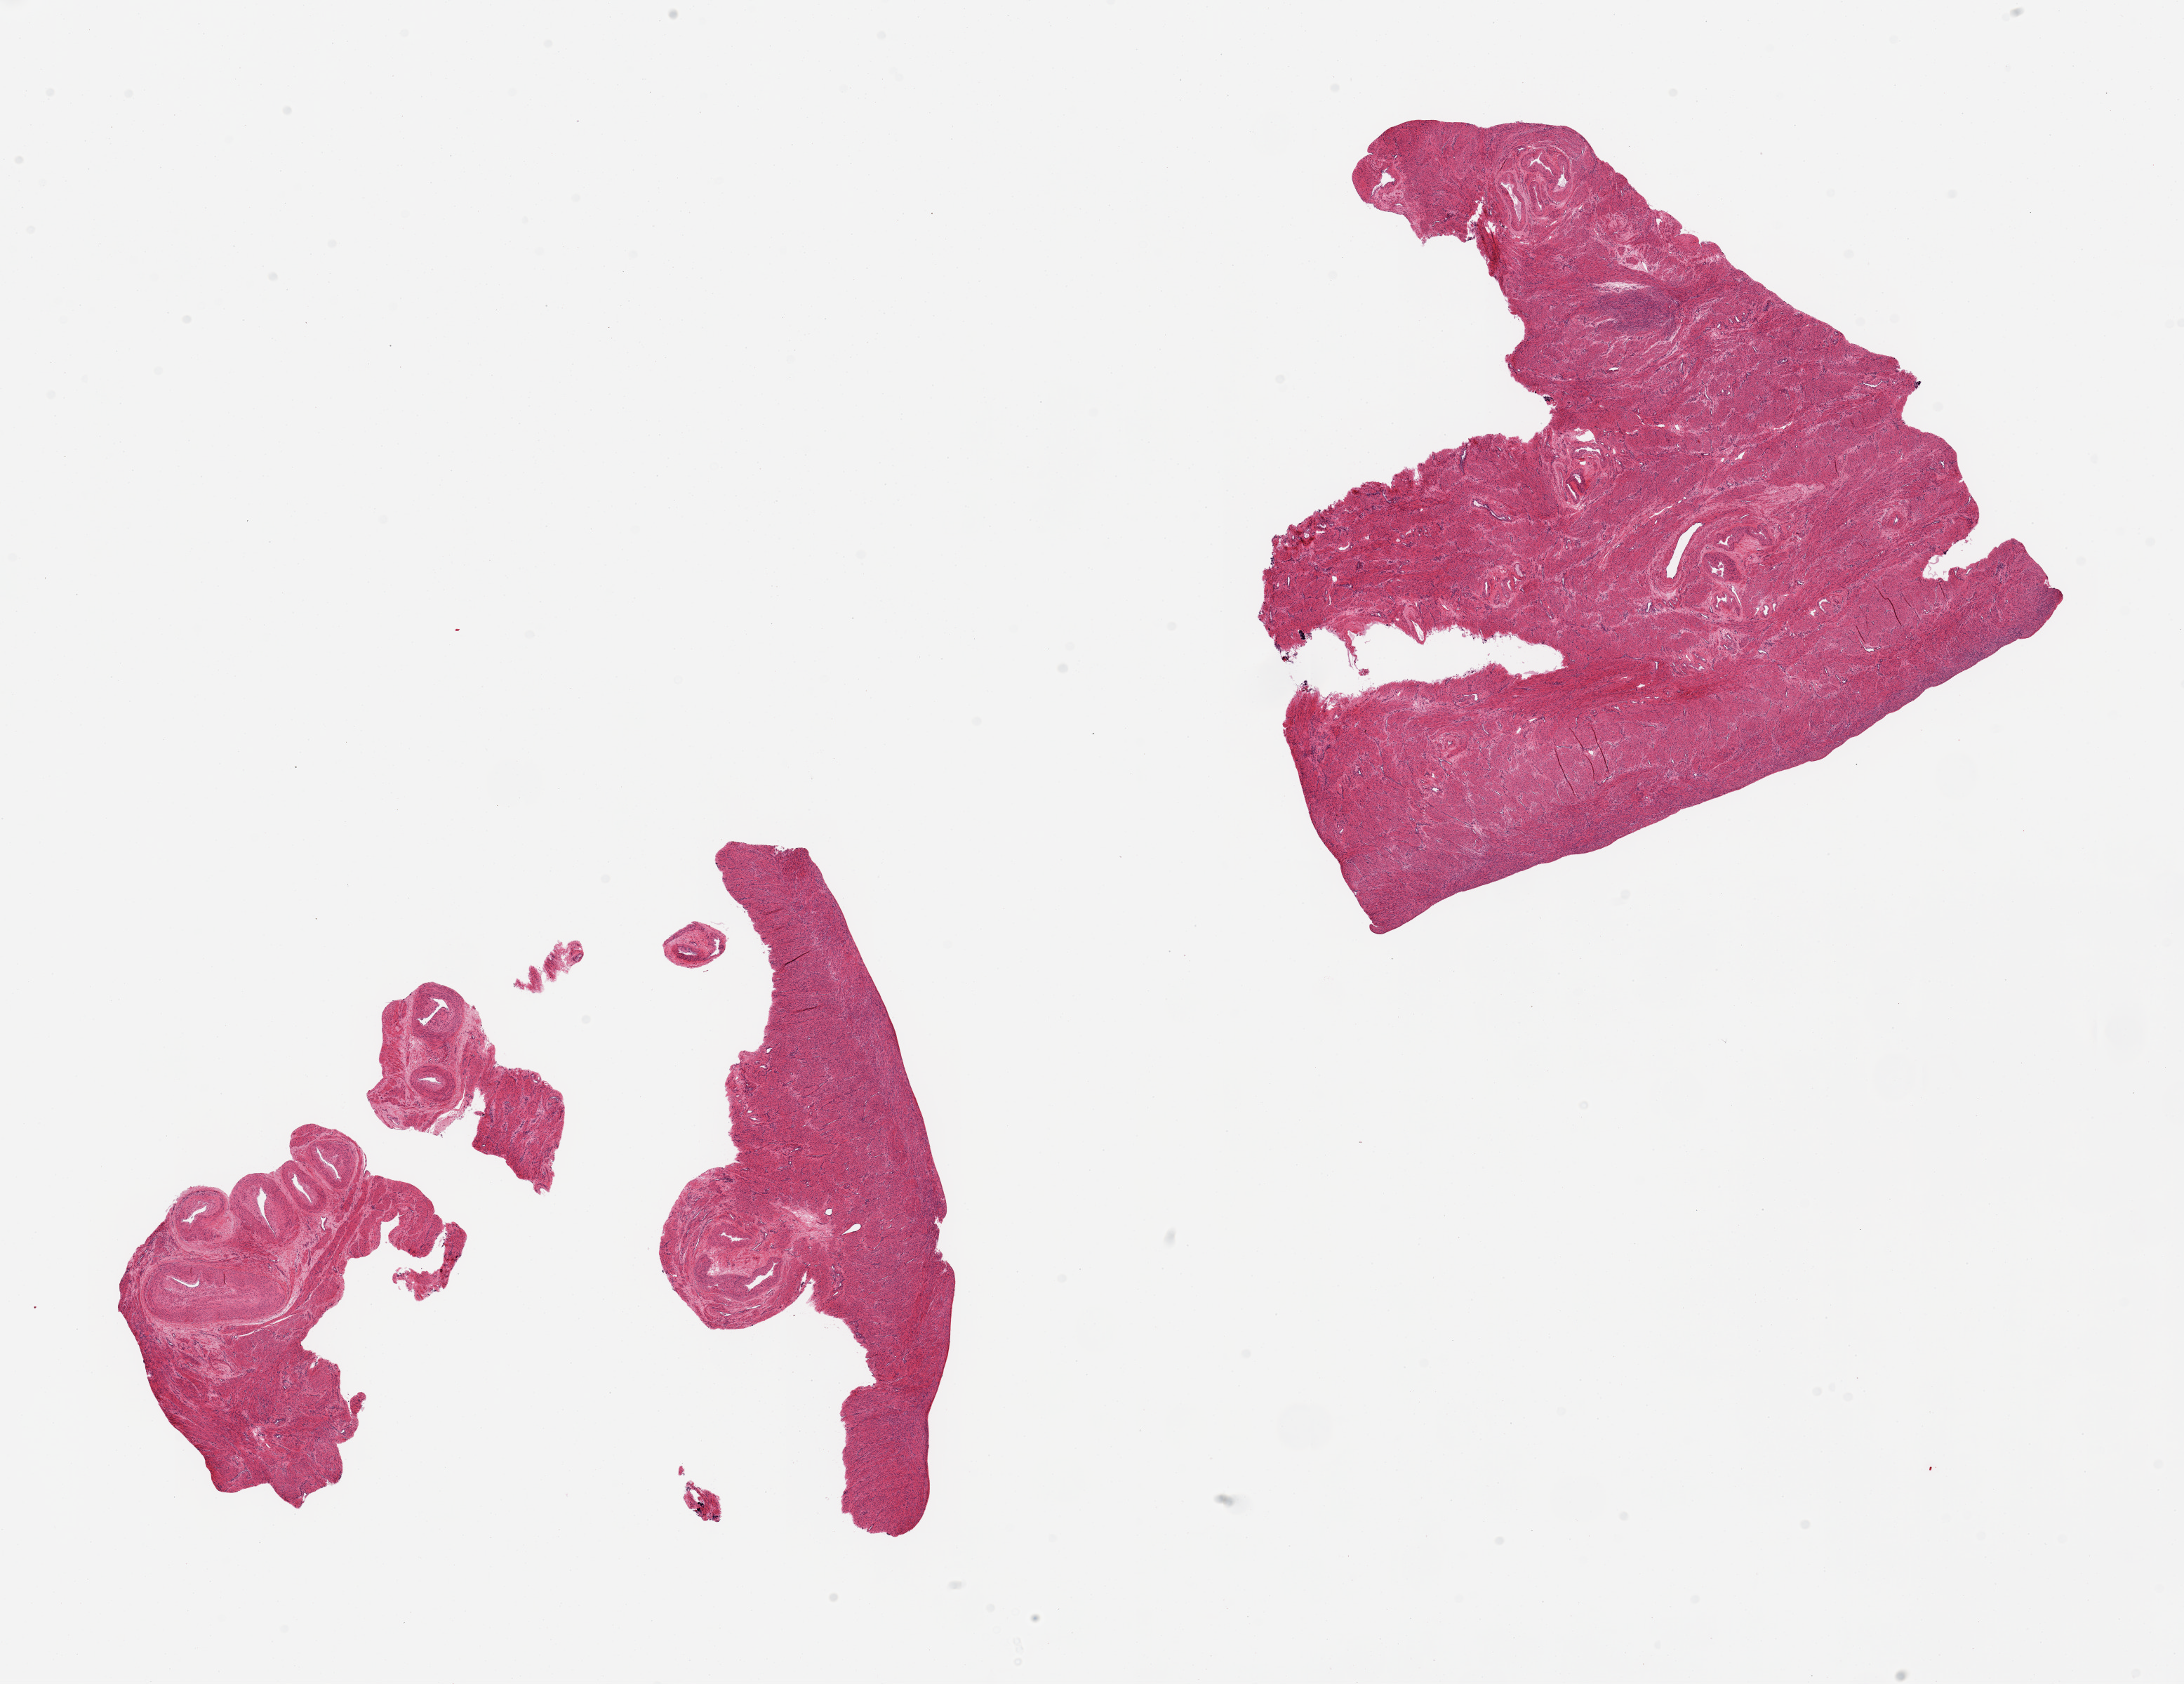
Digitized hematoxylin and eosin (H&E)-stained section, a low-resolution overview of the entire scanned area, about 24.6 x 19.0 mm (slide scanned at 20x), PAXgene-fixed paraffin-embedded (PFPE) section, section of uterus (target tissue), tissue donor sample. Donor: female.
Reviewer comment on this tissue sample: 2 pieces; myometrium only.